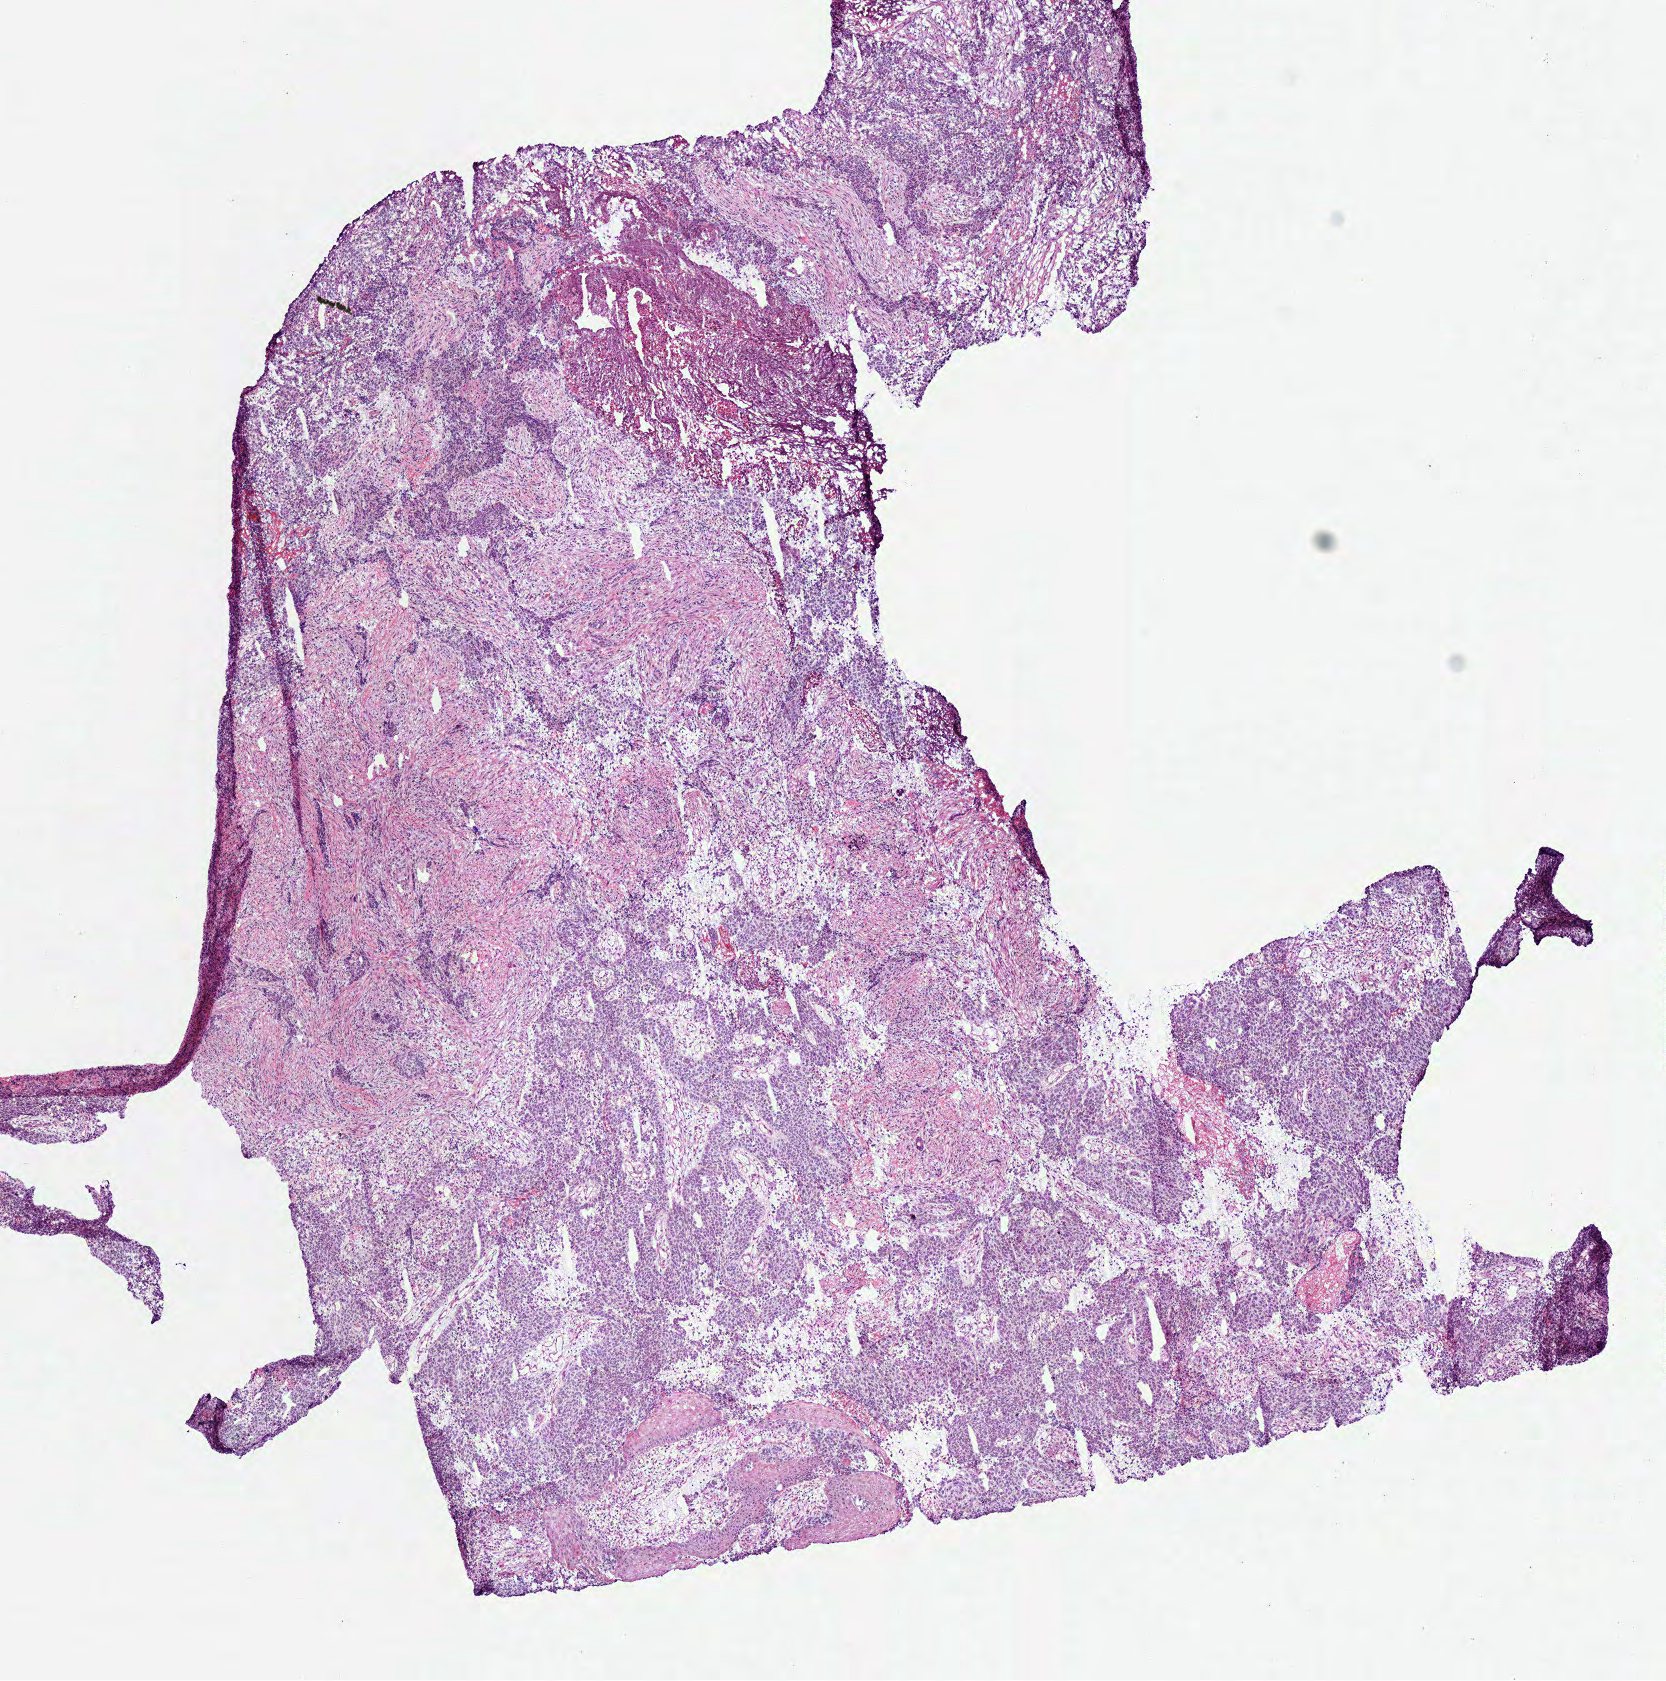
Whole-slide histology image, Hematoxylin and eosin (H&E) stained — low-resolution overview of the scanned area, about 6.6 x 6.6 mm (from a 40x scan); frozen section; head and neck, primary tumour sample. Patient: male, age at initial diagnosis 75 years. Histologic grade: G2 (moderately differentiated). Composition of this section per pathologist review: tumour cells 70%, tumour nuclei 90%, normal cells 0%, stromal cells 28%, necrosis 2%. Inflammatory infiltration, as recorded: lymphocyte infiltration 2%, neutrophil infiltration 2%.
Diagnosis: Squamous cell carcinoma, NOS (base of tongue, NOS).